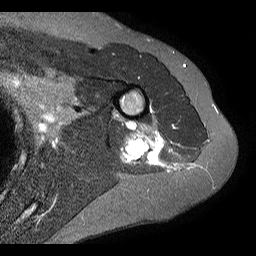
MRI of an extremity soft-tissue mass, one axial slice; position 5 of 20 along the scan axis; STIR; 4 mm slice thickness; 256 × 256 image matrix, field of view 150 × 150 mm. Female patient. From the clinical record (not read from this slice): histological type: malignant fibrous histiocytoma; grade: low; site of the primary tumour: left arm.
Structures marked on this image (expert manual segmentation):
- gross tumour volume (mass): box from (x=121, y=122) to (x=163, y=168) px